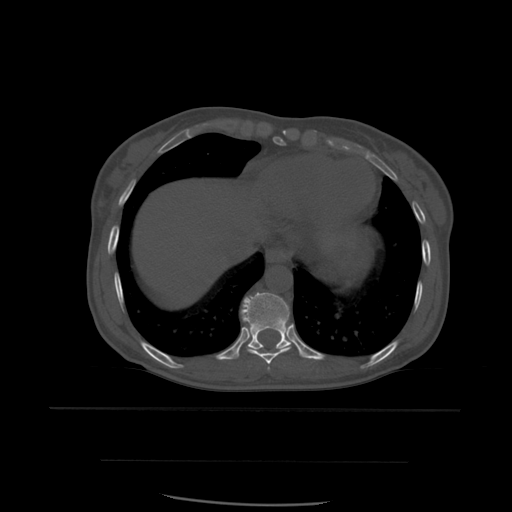
CT including the spine, one axial slice; slice 326 of 574 in the series (ordered by position); bone window (W 1800 / L 400 HU); 1.25 mm slice thickness; 512 × 512 image matrix. Patient age 48 years. From the clinical record (not read from this slice): primary cancer: lung; vertebrae with lytic lesions (as recorded): T11.
Outlined on this slice (semi-automatic segmentation, software-assisted and operator-edited):
- T10 vertebra: bounding box (x1, y1, x2, y2) in pixels: (241, 292, 291, 350)
- T8 vertebra: (268, 367, 271, 371)
- T9 vertebra: (244, 321, 292, 365)